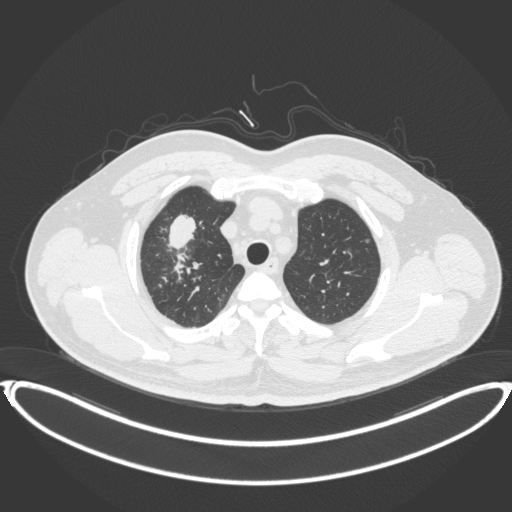
Chest CT, one axial slice. Position 317 of 399 along the scan axis. Reconstruction kernel B31f. 120 kVp. Lung window (W 1500 / L -600 HU). 1 mm slice thickness. 512 × 512 image matrix, field of view 445 × 445 mm. Male patient, age 53 years. Case-level facts recorded for this patient, not image findings: clinical TNM (as recorded): T2a N0 M0.
Annotated regions visible in this slice (bounding box drawn by a radiologist):
- lung tumour (recorded histology: adenocarcinoma): box from (x=162, y=207) to (x=198, y=250) px